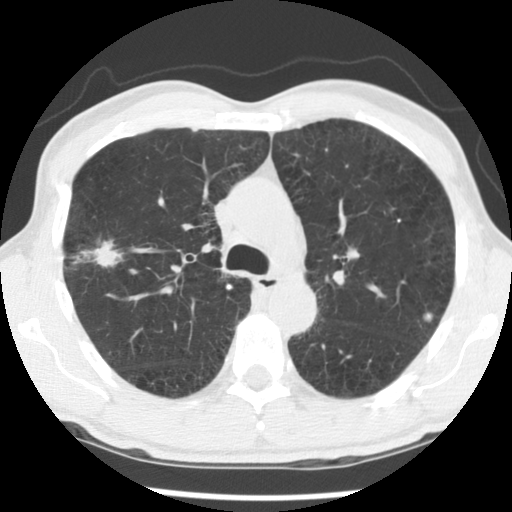
Chest CT (low-dose screening protocol), one axial image. Second screening round (one year after baseline). Lung window (W 1500 / L -600 HU). 2.5 mm slice thickness. Standard (soft-tissue) reconstruction kernel (STANDARD). 140 kVp. Slice 88 of 138 in the series. Male, age 56 years at enrolment. Current smoker at enrolment.
Expert reader's lesion annotation, box from (x=52, y=231) to (x=138, y=292) px. Reader record for this screening exam (exam-level; its link to the box is not recorded): non-calcified nodule or mass ≥4 mm, right upper lobe, 30 × 18 mm, spiculated (stellate) margins, mixed attenuation, pre-existing on the prior screen: yes; interval growth: yes. Official screen result: positive, other. Lung cancer was diagnosed 326 days after this screen: squamous cell carcinoma, NOS, right upper lobe, right middle lobe, moderately differentiated (G2), stage IB (AJCC 6th edition), 70 mm at pathology.